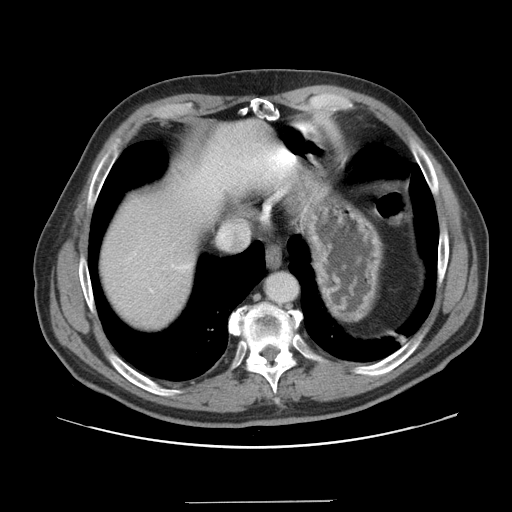
Contrast-enhanced abdominal CT, one axial slice. Slice 138 of 151 in the series (ordered by position). 120 kVp. Intravenous contrast given. Soft-tissue window (W 400 / L 40 HU). 2.5 mm slice thickness. 512 × 512 image matrix. Male patient, age 63 years. Case-level facts recorded for this patient, not image findings: diagnosis: colorectal cancer liver metastases, imaged before liver resection; multiple liver metastases: no; largest metastasis: 2.1 cm; disease in both lobes: no.
Structures marked on this image (expert manual segmentation):
- hepatic veins: bounding box (x1, y1, x2, y2) in pixels: (221, 234, 225, 239)
- liver: (98, 119, 291, 331)
- planned liver remnant (the part of the liver to remain after resection): (98, 154, 226, 331)